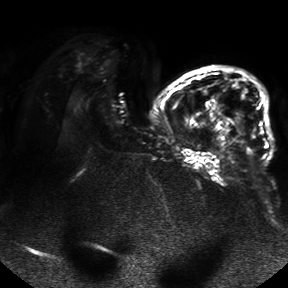
Breast MRI, one axial slice; slice 23 of 50 in the series (ordered by position); diffusion-weighted series; image 2 of 4 stored at this slice position (different b-values; order by instance number); 1.5 T; 4 mm slice thickness; 288 × 288 image matrix. Female patient.
Annotated regions visible in this slice (expert manual segmentation):
- tumour on diffusion-weighted imaging: bounding box (x1, y1, x2, y2) in pixels: (234, 112, 248, 144)